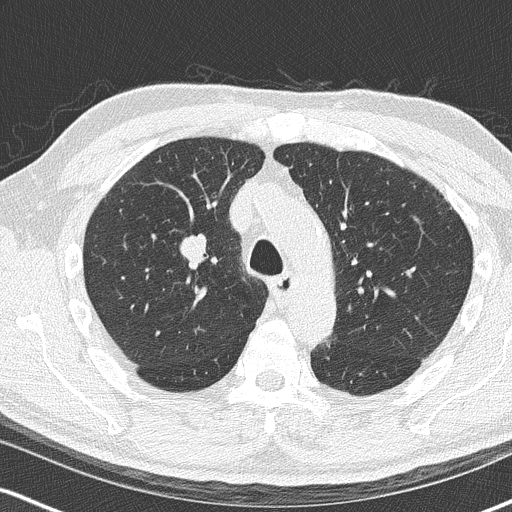
Chest CT (low-dose screening protocol), one axial image; second annual screen; lung window (W 1500 / L -600 HU); 512 × 512 image matrix, field of view 320 × 320 mm. Male, age 68 years at enrolment. Current smoker at enrolment.
Expert reader's lesion annotation, bounding box (x1, y1, x2, y2) in pixels: (152, 223, 217, 286). Reader record for this screening exam (exam-level; its link to the box is not recorded): non-calcified nodule or mass ≥4 mm, right upper lobe, 18 × 15 mm, smooth margins, soft tissue attenuation, pre-existing on the prior screen: no. Official screen result: positive, change unspecified: nodule(s) >= 4 mm or enlarging nodule(s), mass(es), or other non-specific abnormalities suspicious for lung cancer. Later outcome: lung cancer diagnosed 136 days after this screen — small cell carcinoma, NOS, right upper lobe, stage IIIB (AJCC 6th edition), 20 mm at pathology.